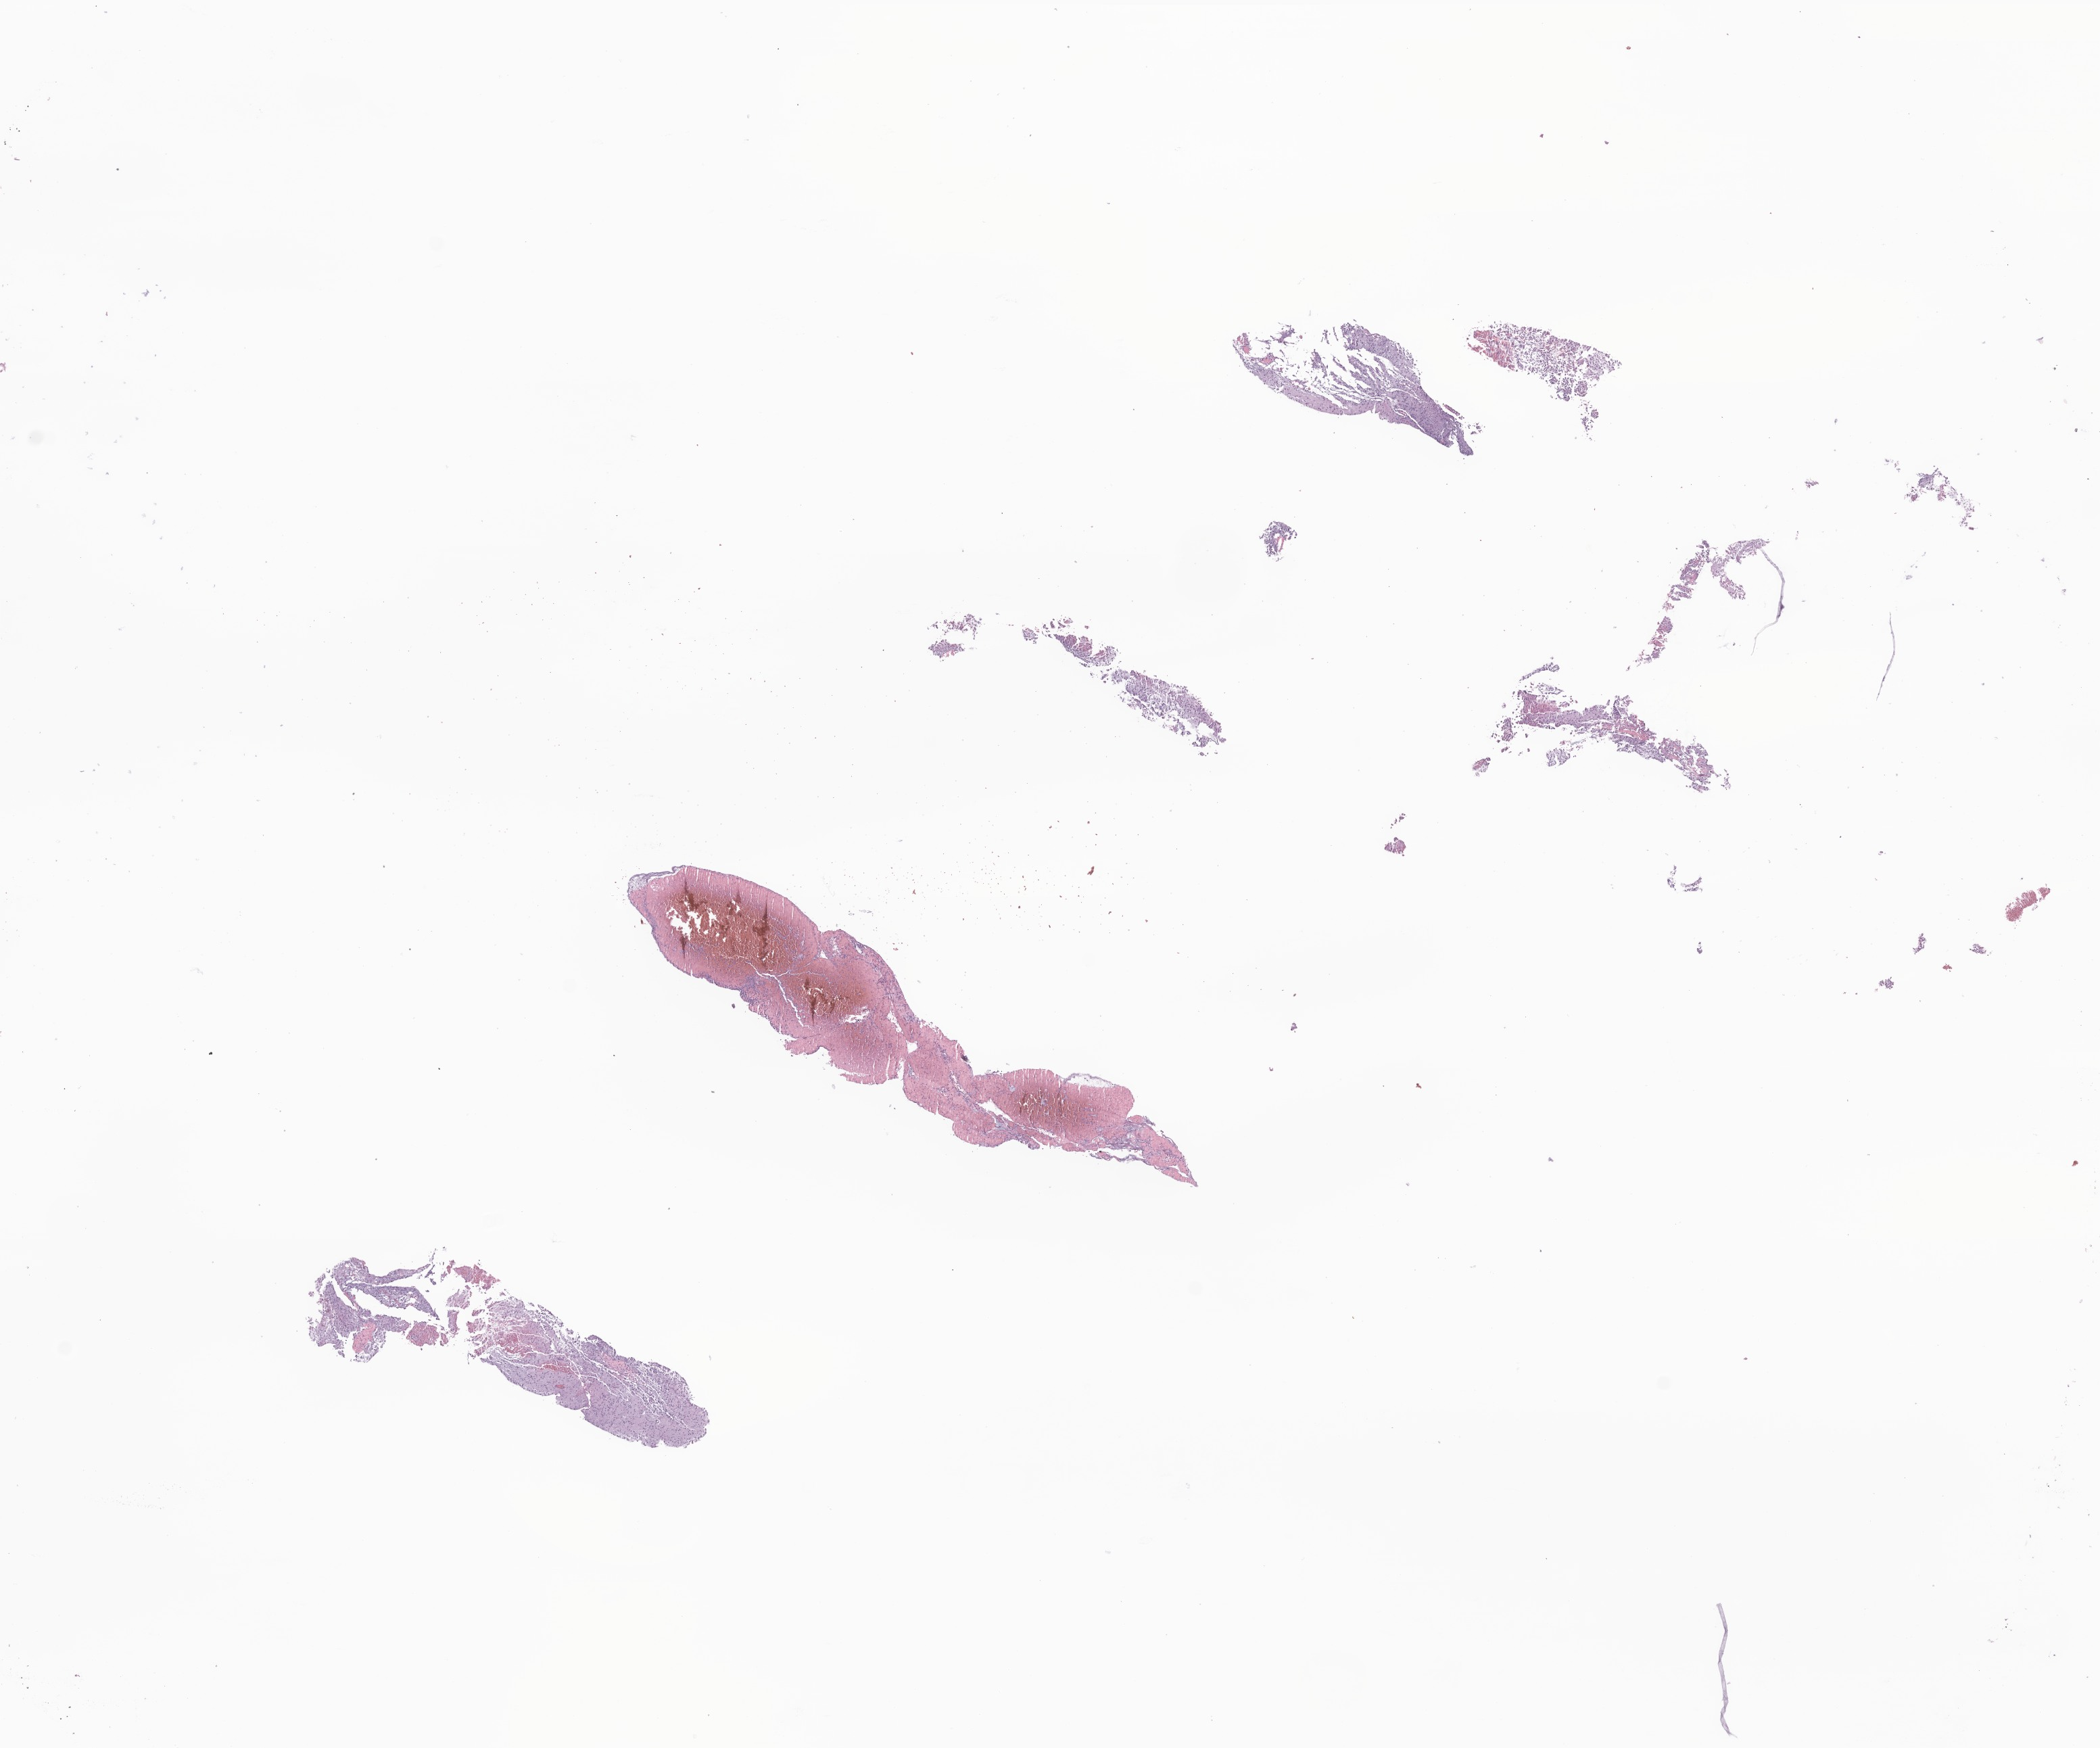
Digitized hematoxylin and eosin (H&E)-stained section of tumor tissue from the brain — whole scanned area (about 13.1 x 10.9 mm) shown as a low-resolution overview, formalin-fixed, paraffin-embedded (FFPE) tissue. Male patient, age 235 months (19 years 7 months).
- diagnosis: Glioma, malignant